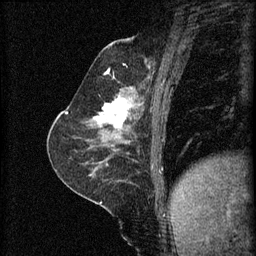
Breast MRI (dynamic contrast-enhanced), one sagittal slice. Slice 27 of 60 in the series (ordered by position). 3 images stored at this slice position (order not interpretable as contrast timing). 1.5 T. TE 4.2 ms, TR 8.2 ms. 2 mm slice thickness. 256 × 256 image matrix, field of view 180 × 180 mm. Female patient, age 59 years.
Structures marked on this image (semi-automatically segmented with operator editing):
- analysis volume of interest (the breast-tissue region the enhancement analysis was run in; not a lesion): bounding box (x1, y1, x2, y2) in pixels: (86, 92, 137, 135)
- tumour enhancement mask (voxels above the 70 % enhancement threshold inside the analysis volume of interest): (94, 96, 131, 129)